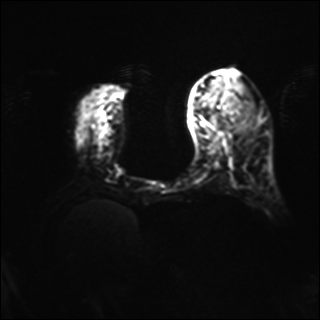
Breast MRI, one axial slice. Position 16 of 40 along the scan axis. Diffusion-weighted series; image 2 of 4 stored at this slice position (different b-values; order by instance number). 1.5 T. 320 × 320 image matrix, field of view 320 × 320 mm. Female patient.
Outlined on this slice (manually delineated by an expert):
- tumour on diffusion-weighted imaging: bounding box <219,97,248,126> (left, top, right, bottom; pixels)